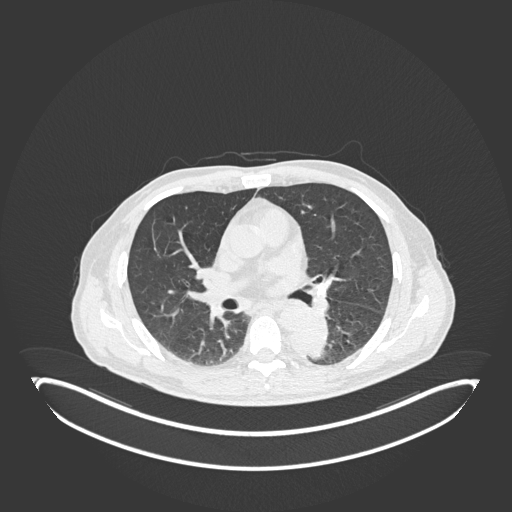
Chest CT, one axial slice. Slice 110 of 251 in the series (ordered by position). Reconstruction kernel B30f. 120 kVp. Lung window (W 1500 / L -600 HU). 1 mm slice thickness. 512 × 512 image matrix. Patient: male, 72 years. From the clinical record (not read from this slice): clinical TNM (as recorded): T2b N0 M1.
Annotated regions visible in this slice (bounding box drawn by a radiologist):
- lung tumour (recorded histology: adenocarcinoma): bounding box <288,312,329,361> (left, top, right, bottom; pixels)